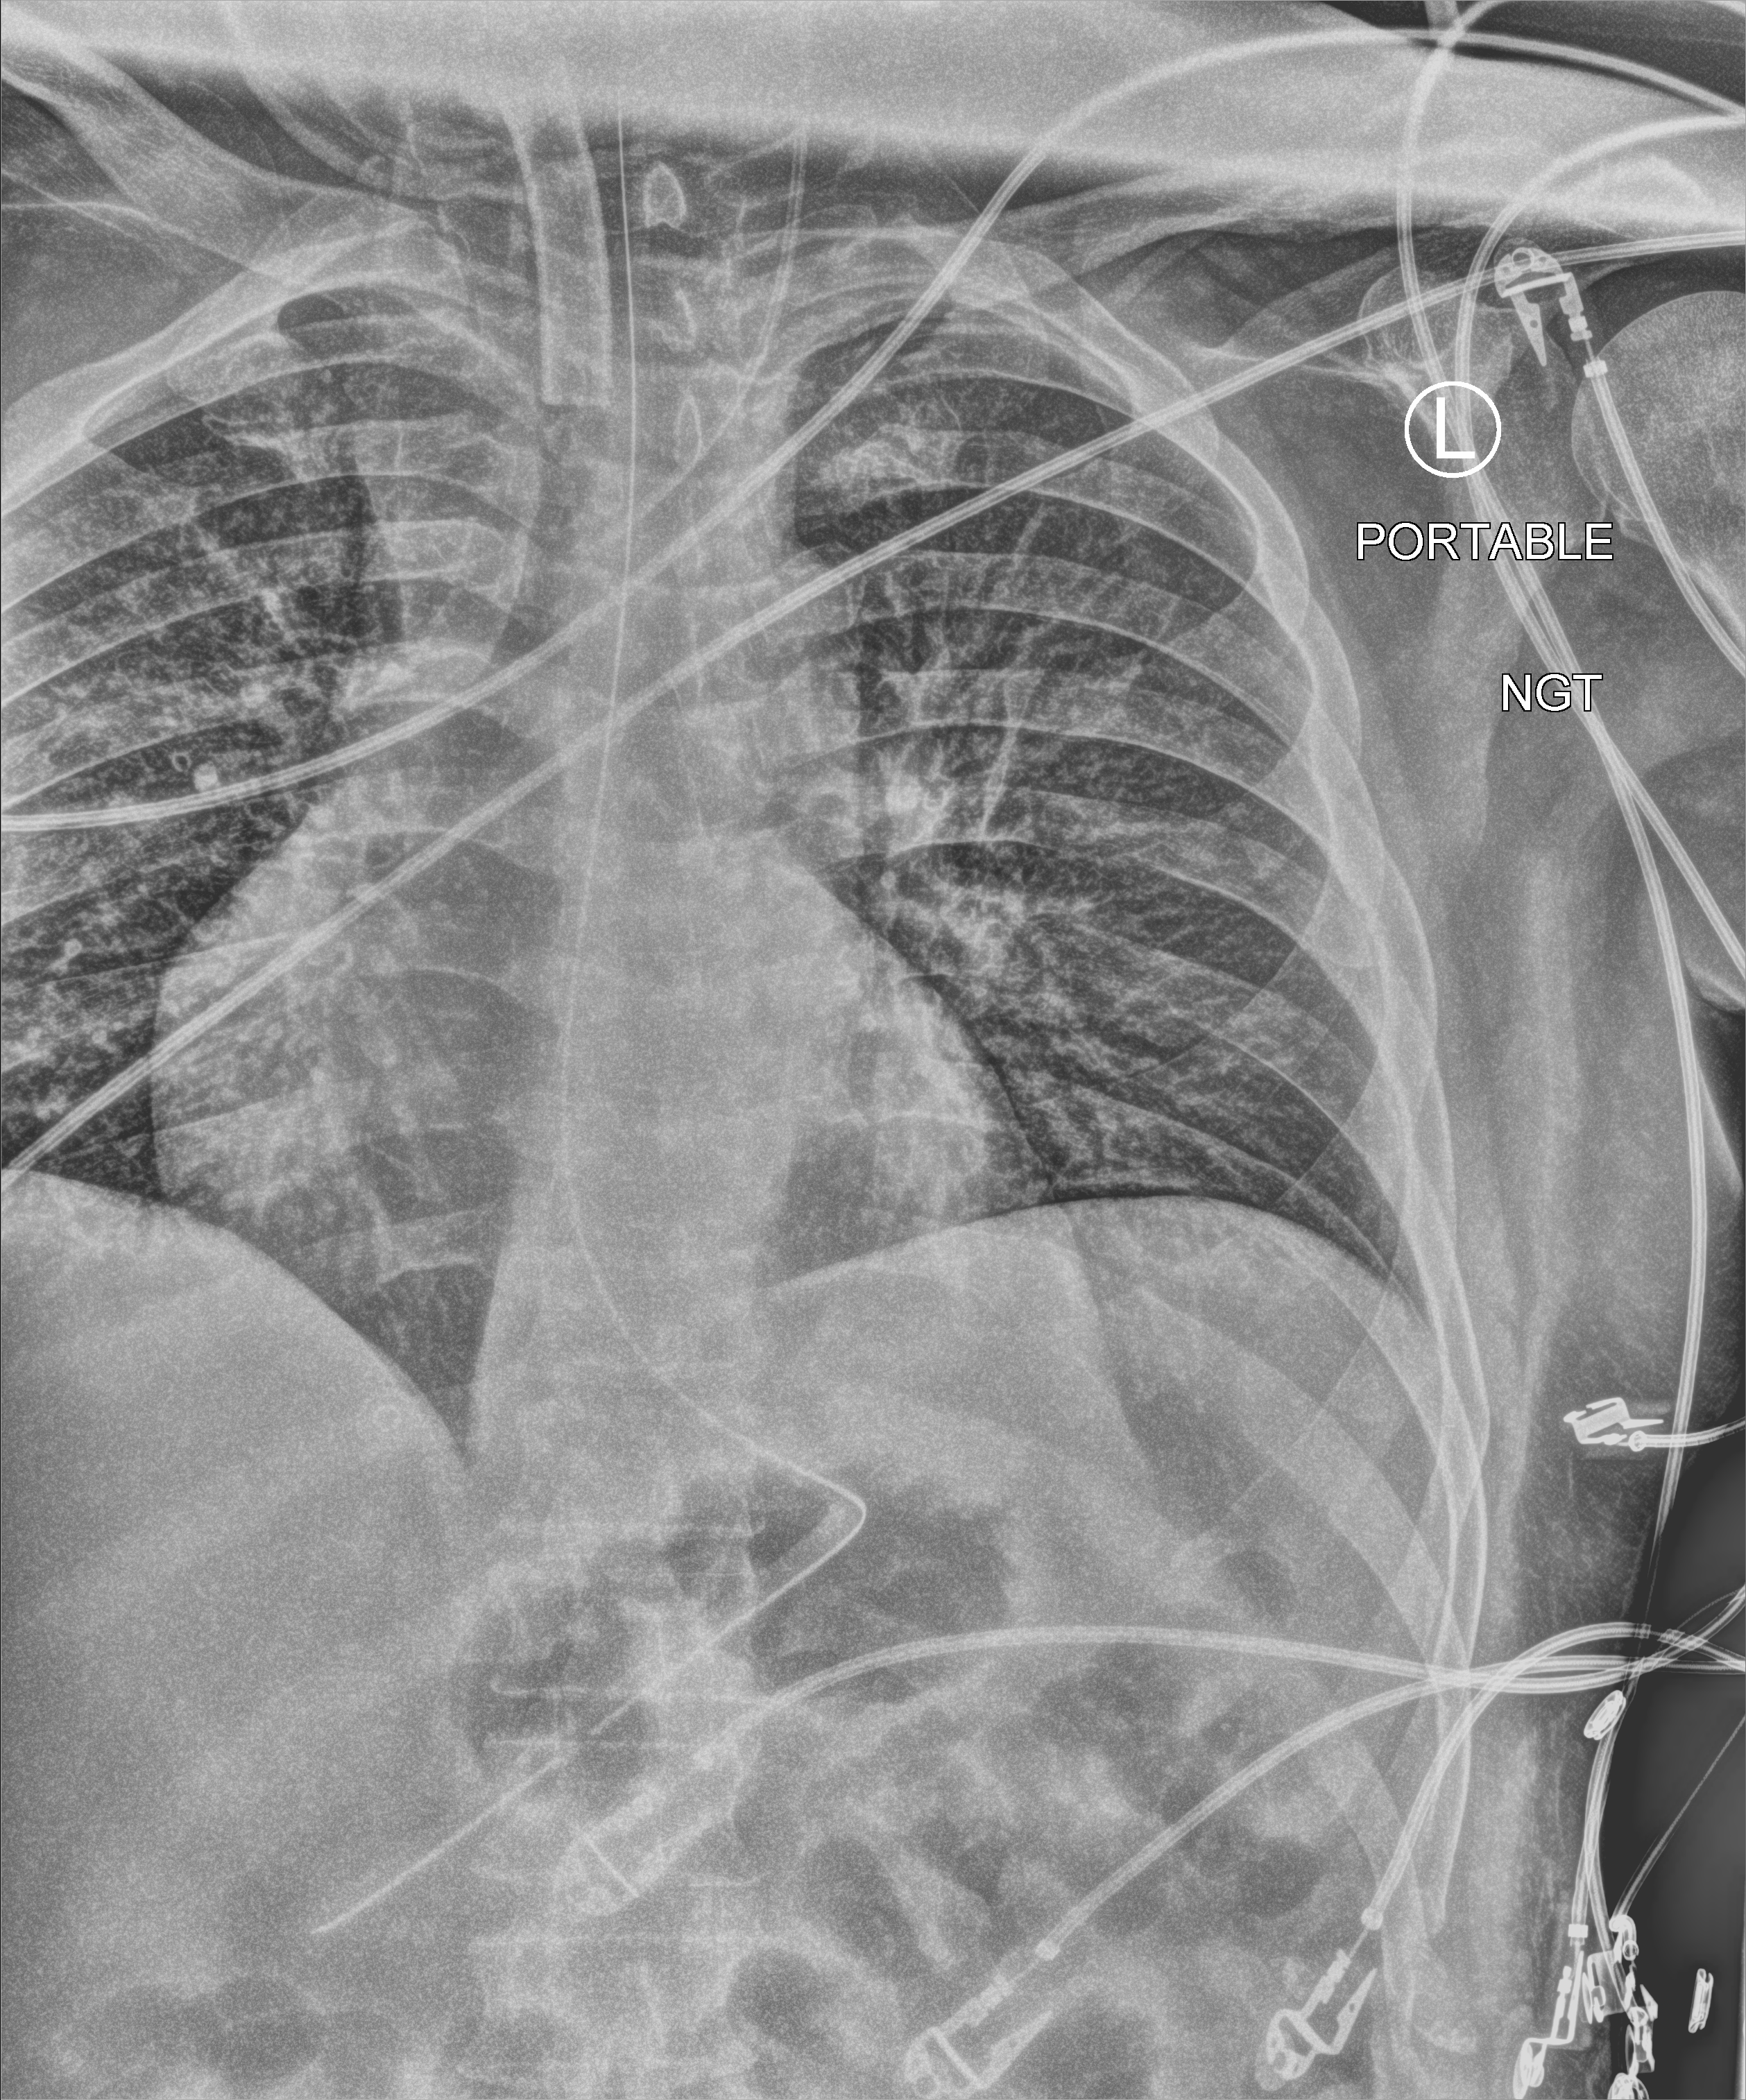
Portable chest radiograph. Patient hospitalised with COVID-19; male, aged 18–59 years.
From the hospital-stay record, not from the radiograph (when in the stay this image was taken is not recorded): admitted to intensive care during this hospital stay: yes; mechanically ventilated during this hospital stay: yes.